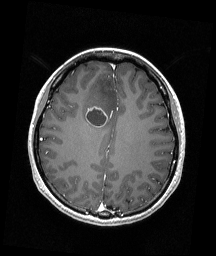
Brain MRI from a brain-tumour surgery series, one axial slice; position 69 of 192 along the scan axis; T1-weighted post-contrast; 1 mm slice thickness; 216 × 256 image matrix. From the clinical record (not read from this slice): histopathology: Astrocytoma; WHO grade: 4; IDH mutation: yes; tumour location: Right Frontal.
Annotated regions visible in this slice (expert manual segmentation):
- tumour: bounding box <85,106,108,127> (left, top, right, bottom; pixels)